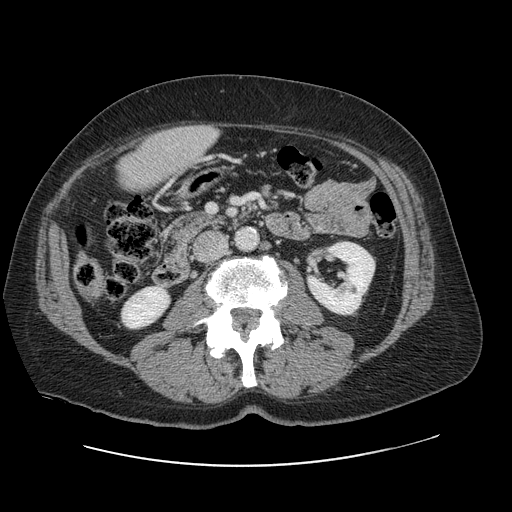
Contrast-enhanced abdominal CT, one axial slice. Position 19 of 138 along the scan axis. Intravenous contrast given. Soft-tissue window (W 400 / L 40 HU). 512 × 512 image matrix, field of view 402 × 402 mm. Male patient, age 71 years. Case-level facts recorded for this patient, not image findings: diagnosis: colorectal cancer liver metastases, imaged before liver resection; multiple liver metastases: no; largest metastasis: 3.3 cm; disease in both lobes: no.
Outlined on this slice (outlined manually by an expert reader):
- liver: bounding box (x1, y1, x2, y2) in pixels: (119, 126, 218, 189)
- planned liver remnant (the part of the liver to remain after resection): (119, 137, 175, 190)